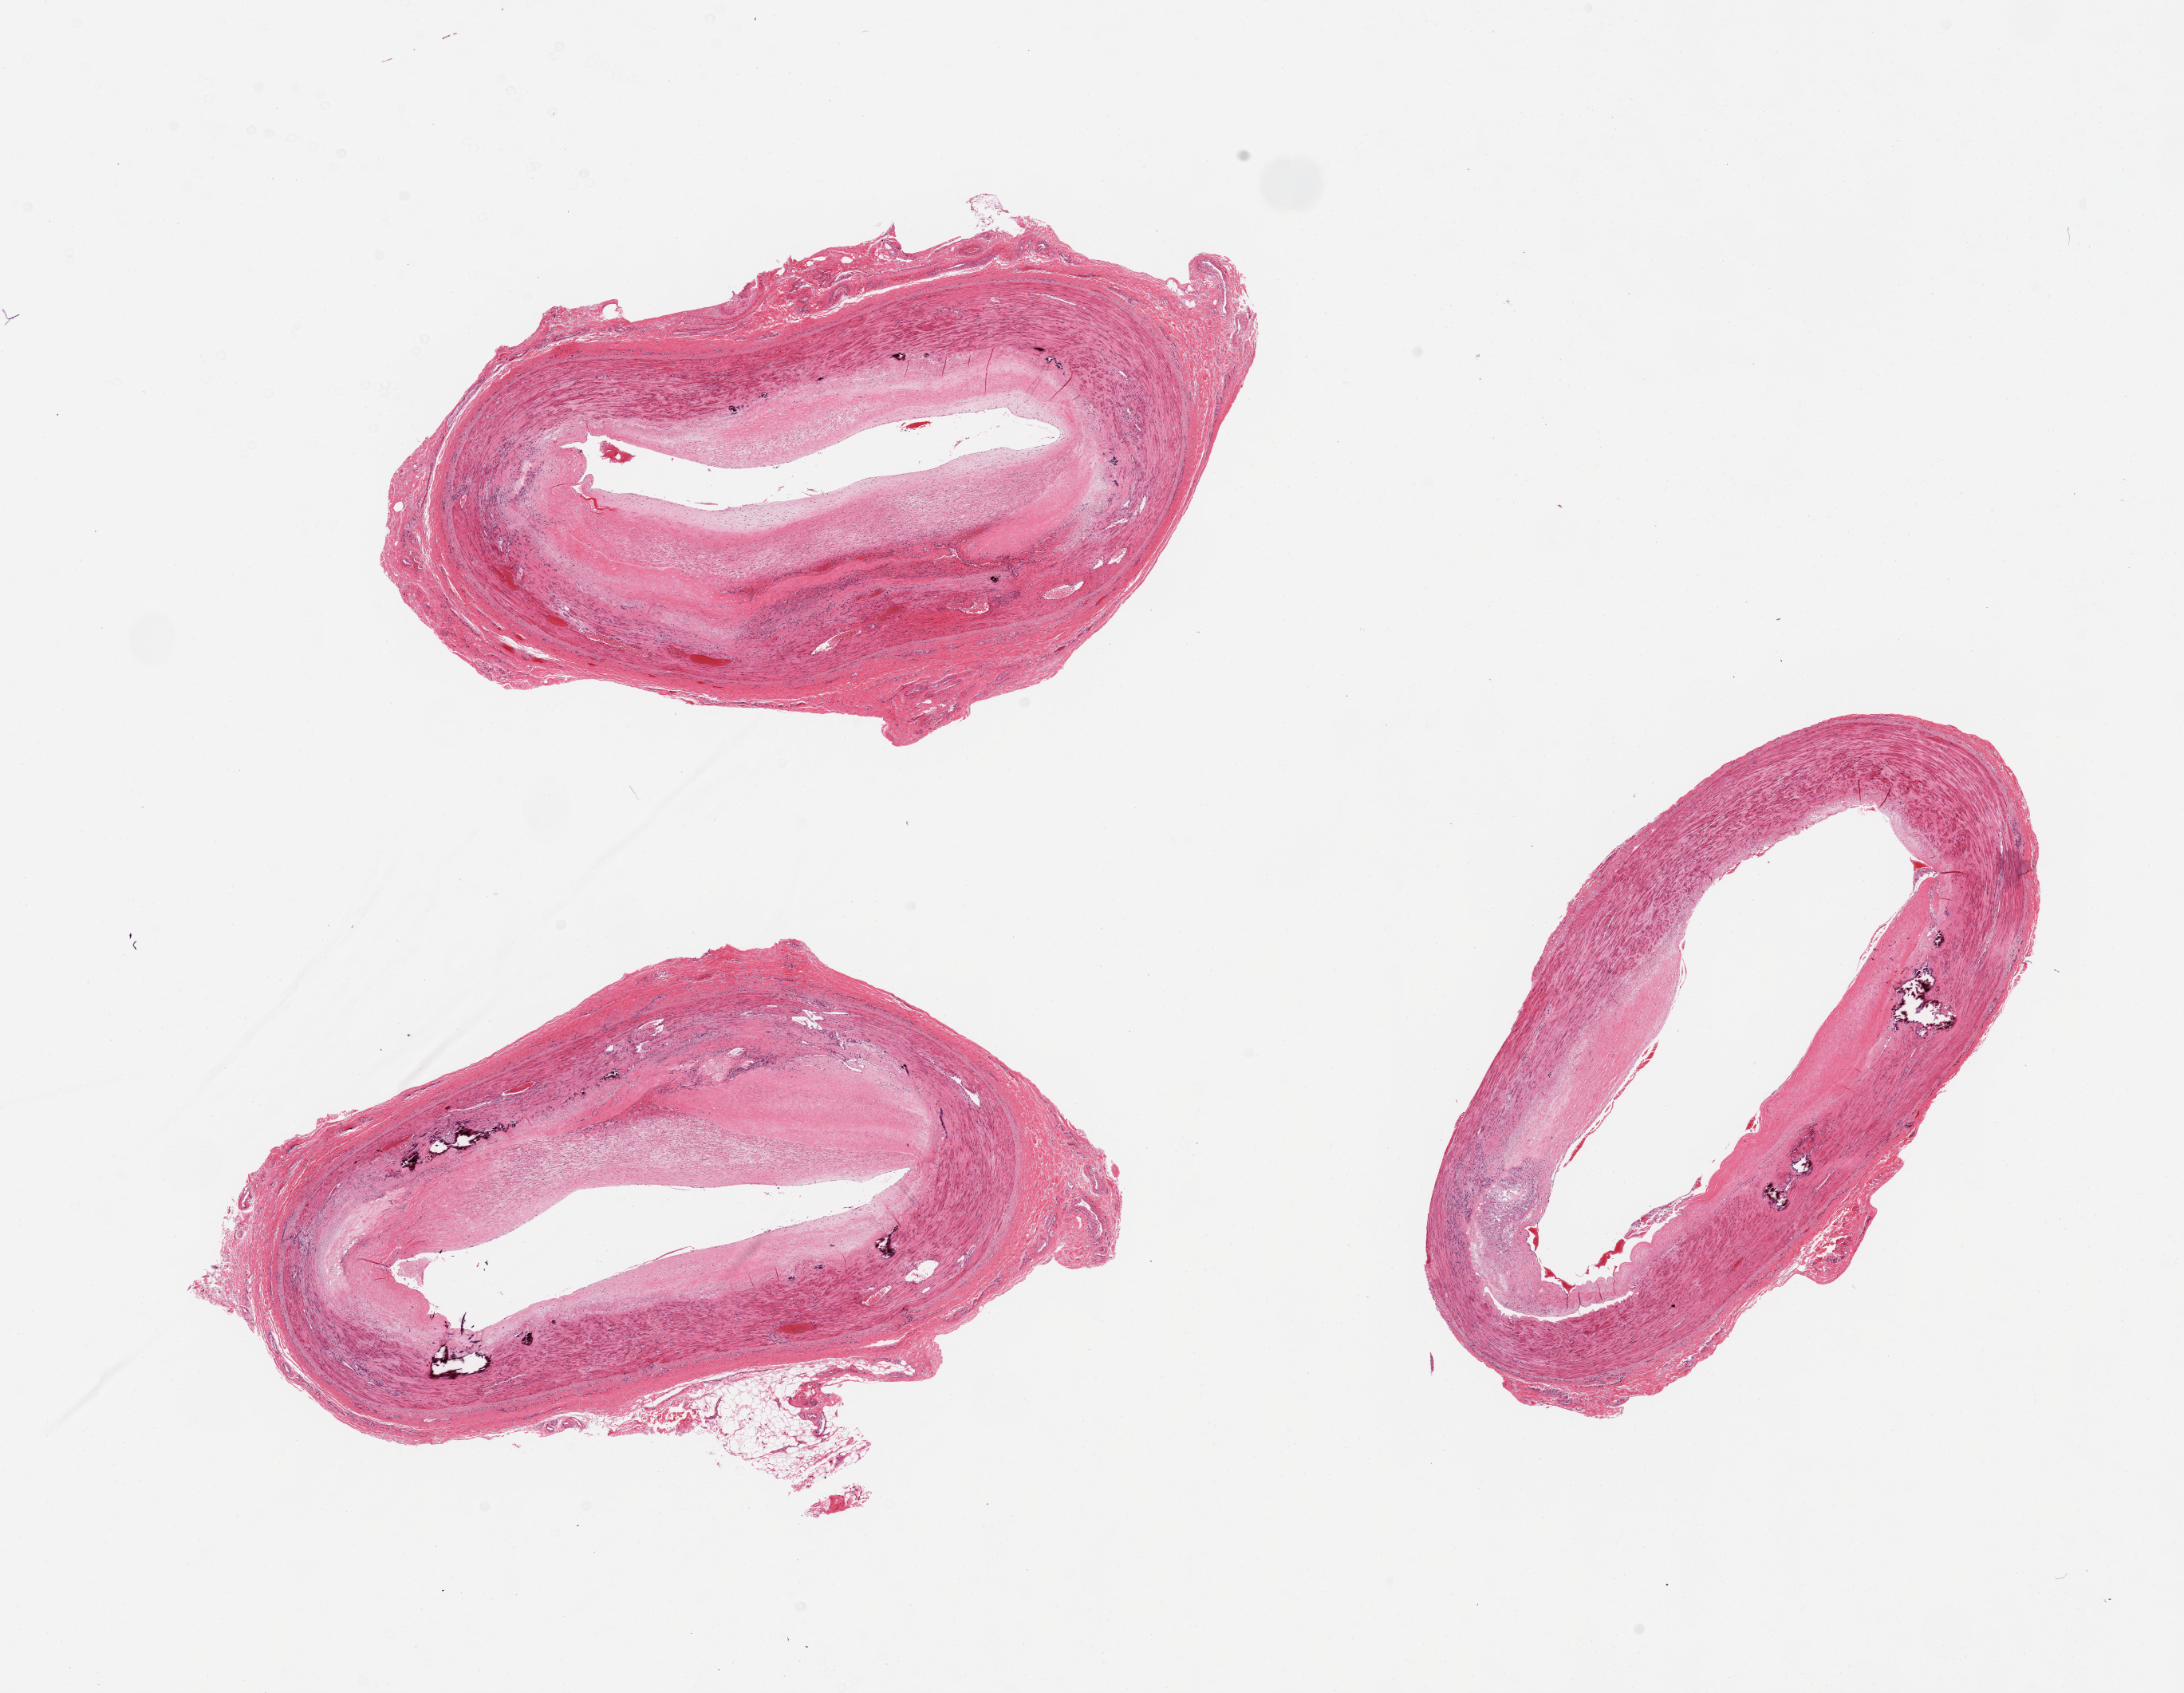
Whole-slide image, haematoxylin and eosin stain, brightfield — shown as a low-resolution overview of the whole scanned area (about 21.7 x 16.8 mm); PAXgene-fixed, paraffin-embedded tissue; target tissue: tibial artery; tissue donor sample. Donor: male.
Pathologist's review note for this sample: 3 pieces, atherosclerosis with narrowing of the lumen by ~50%, medial calcification.